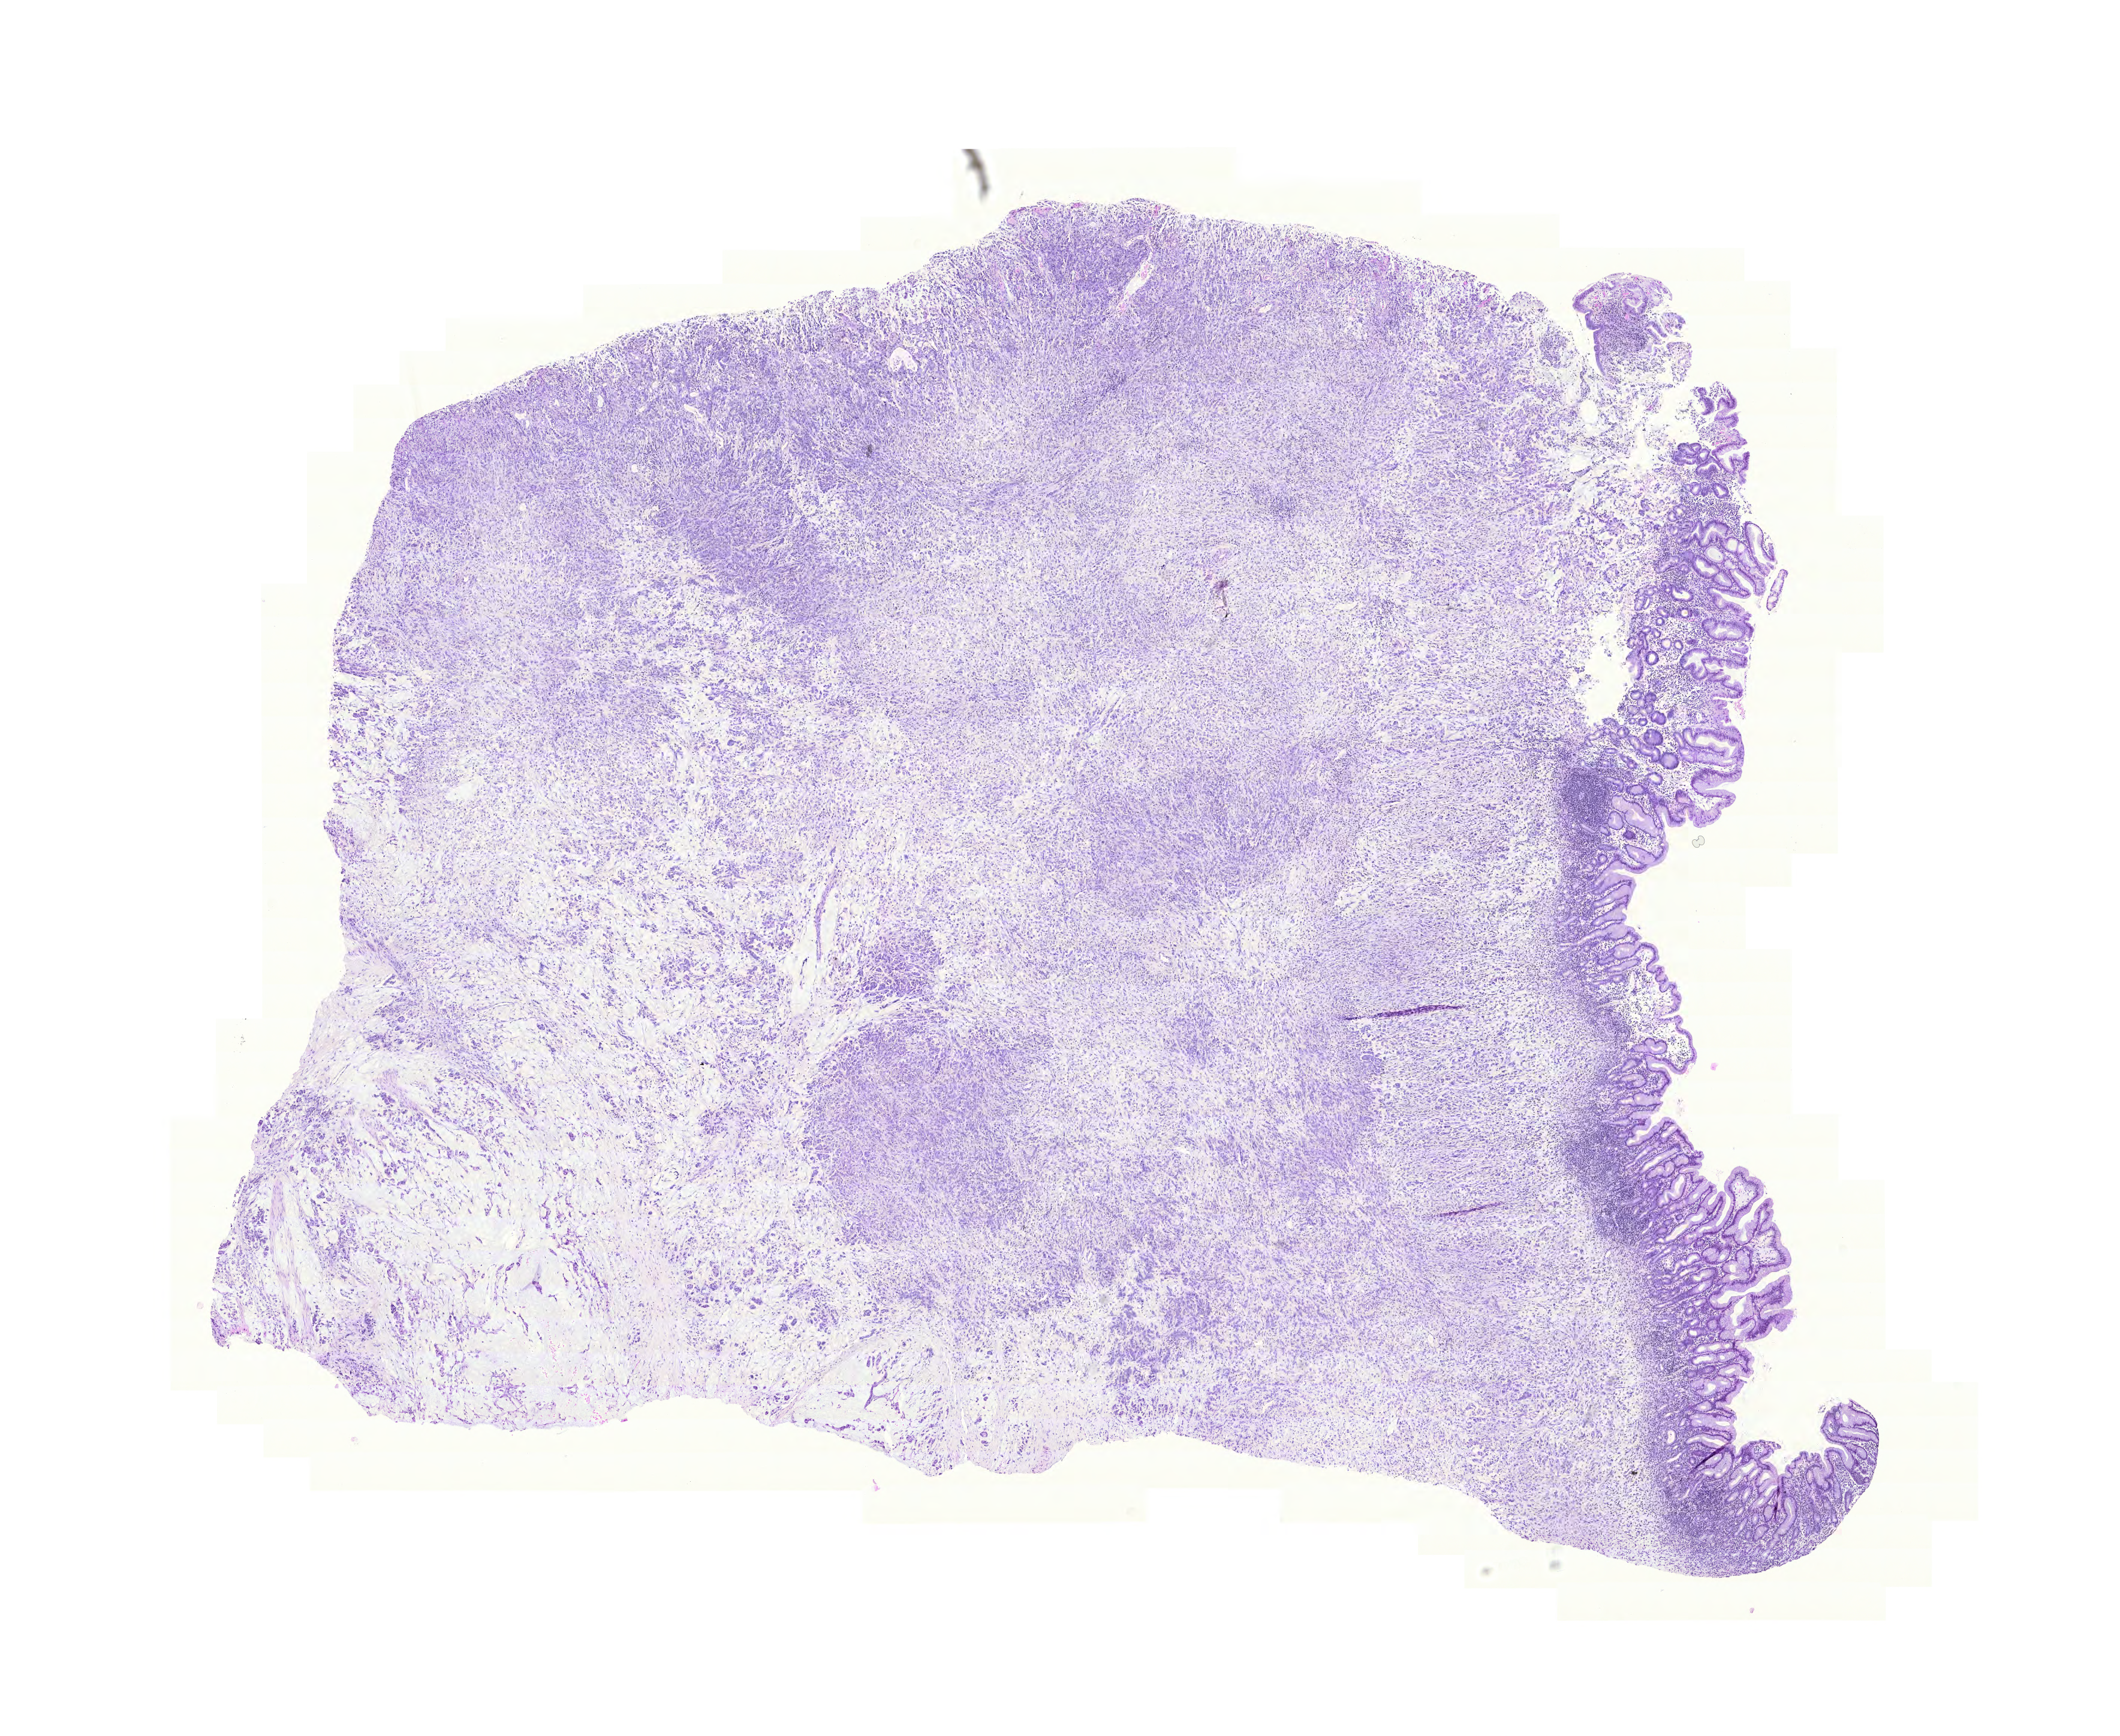
Digitized Hematoxylin and eosin (H&E) stained tissue section (whole slide), shown as a low-resolution overview of the whole scanned area (about 13.2 x 10.8 mm, from a 20x scan), FFPE section, stomach, primary tumour sample. Female, age 67 years at initial diagnosis. Histologic grade: G3 (poorly differentiated).
Histologic diagnosis: Carcinoma, diffuse type (gastric antrum). AJCC pathologic stage: IV (7th edition).